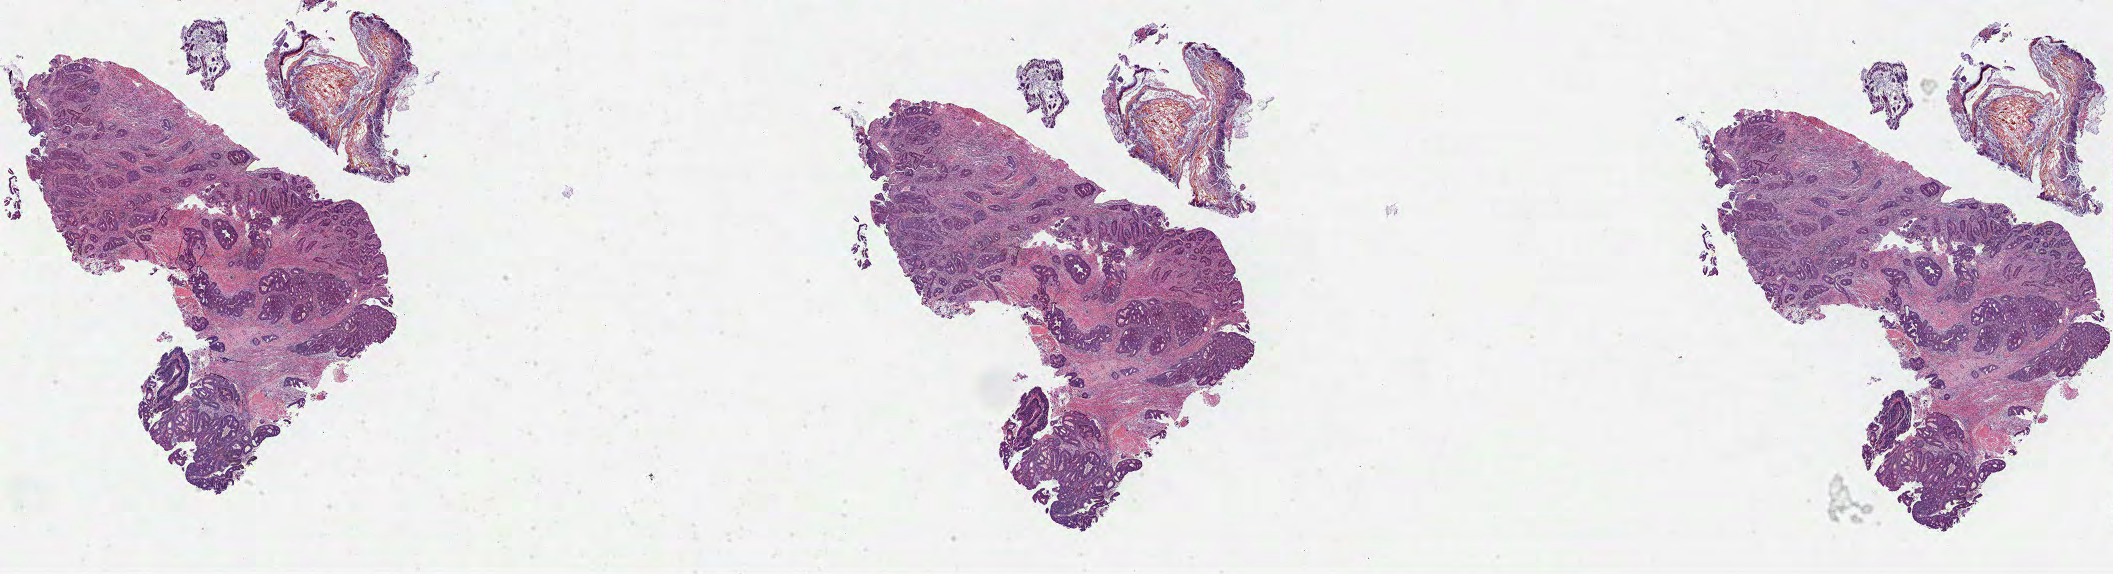
H&E-stained whole-slide image, a low-resolution overview of the entire scanned area, about 34.1 x 9.3 mm, FFPE section, colon, primary tumour sample. Patient: male, age at initial diagnosis 62 years.
AJCC pathologic stage: IIA. TNM: T3 N0 M0. Pathologic diagnosis: Adenocarcinoma, NOS (descending colon). Lymph nodes positive (case pathology): 0 of 46 examined.